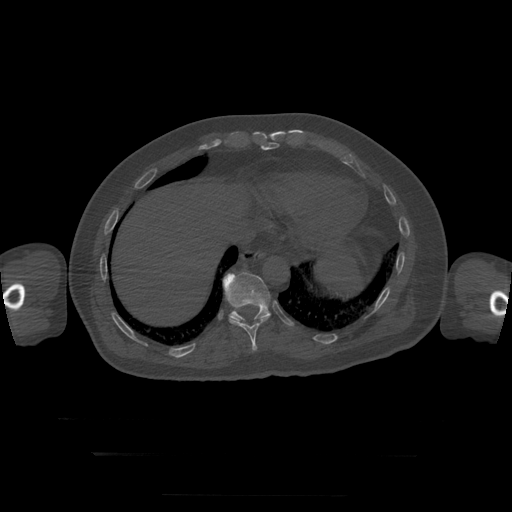
CT including the spine, one axial slice; position 113 of 397 along the scan axis; 120 kVp; bone window (W 1800 / L 400 HU); 1.25 mm slice thickness; 512 × 512 image matrix, field of view 510 × 510 mm. Patient age 73 years. Case-level facts recorded for this patient, not image findings: primary cancer: prostate.
Outlined on this slice (semi-automatically segmented with operator editing):
- T10 vertebra: bounding box (x1, y1, x2, y2) in pixels: (229, 316, 270, 352)
- T11 vertebra: (223, 272, 271, 323)